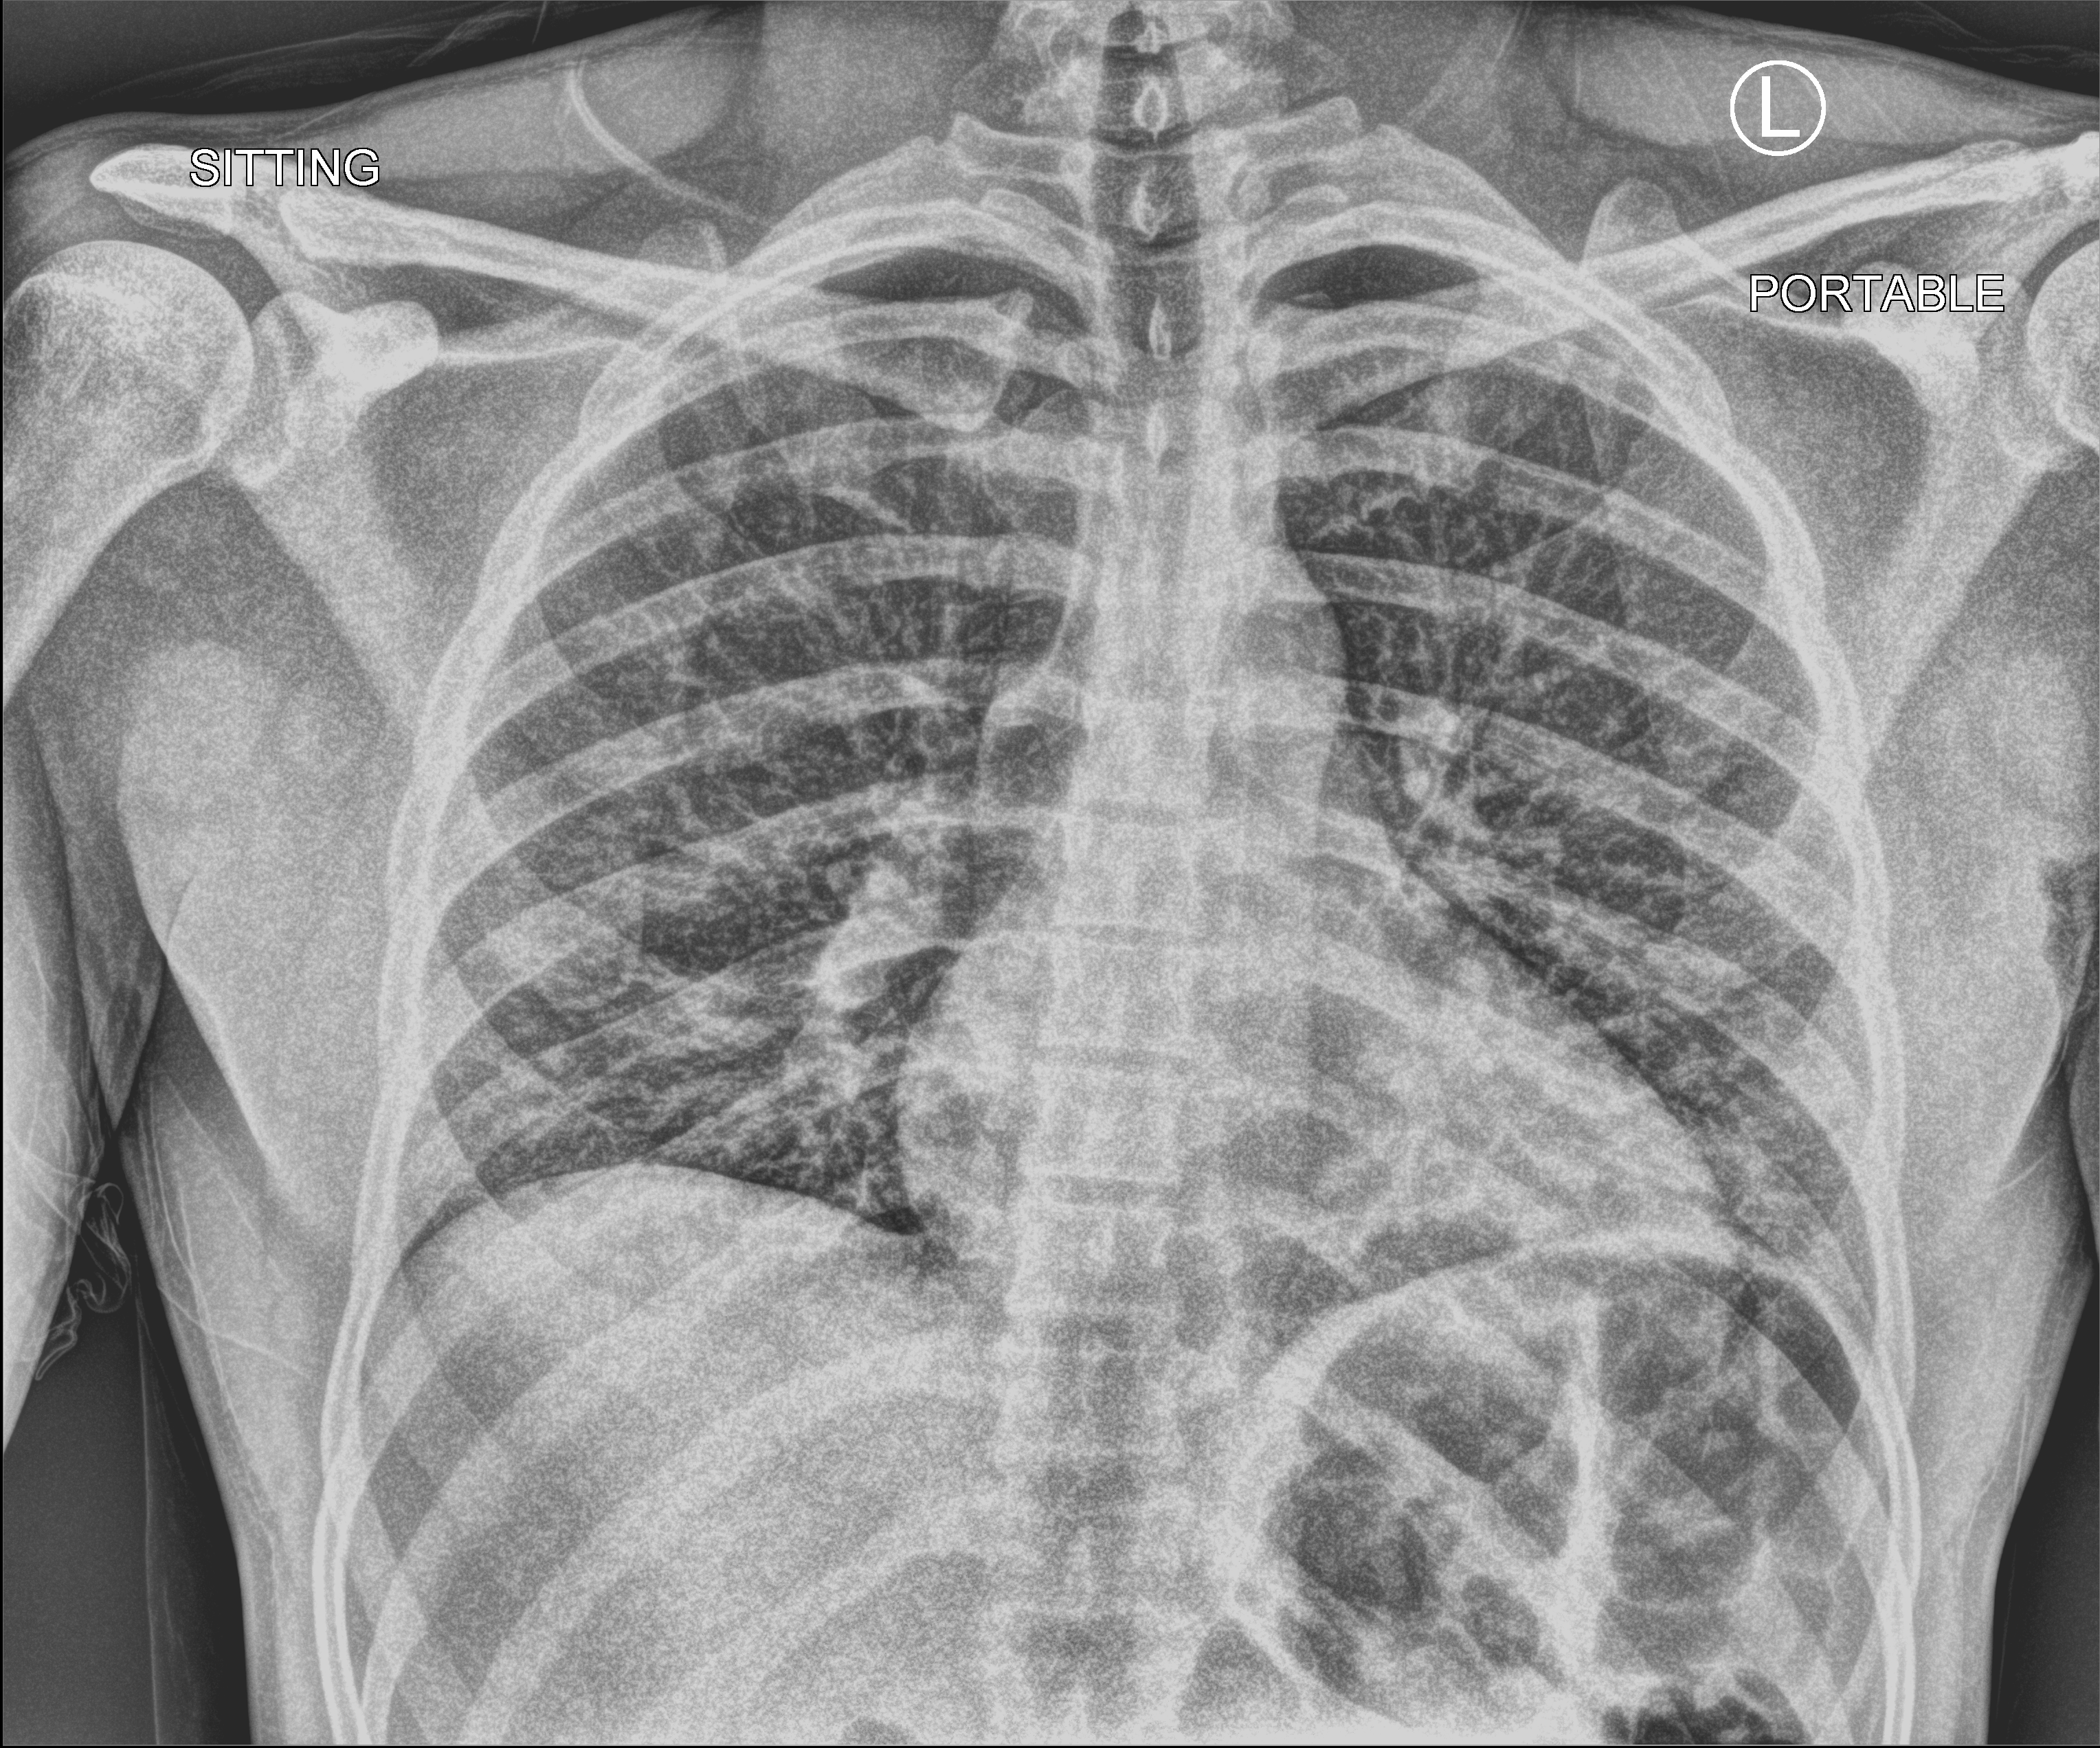
Bedside chest radiograph (computed radiography). Male patient hospitalised with COVID-19, age 18–59 years.
Admission-level facts for this patient (not findings on this image; timing relative to this image not recorded): mechanically ventilated during this hospital stay: no; hypertension (admission record): no; admitted to intensive care during this hospital stay: no.